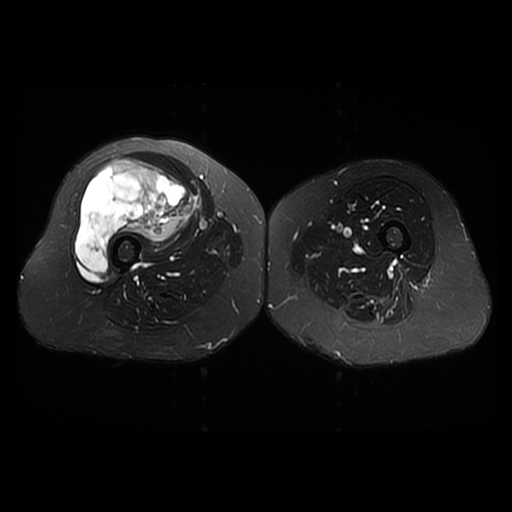
MRI of an extremity soft-tissue mass, one axial slice; slice 23 of 42 in the series (ordered by position); T2-weighted fat-saturated; 6 mm slice thickness; 512 × 512 image matrix, field of view 440 × 440 mm. Female patient. From the clinical record (not read from this slice): histological type: pleiomorphic undifferentiated sarcoma; grade: high; site of the primary tumour: right quadricep.
Structures marked on this image (manually delineated by an expert):
- gross tumour volume including surrounding oedema: bounding box (x1, y1, x2, y2) in pixels: (74, 158, 197, 272)
- gross tumour volume (mass): (74, 158, 197, 272)